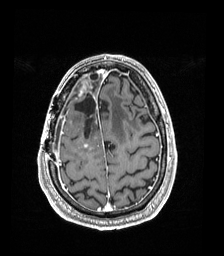
Brain MRI from a brain-tumour surgery series, one axial slice. Slice 45 of 192 in the series (ordered by position). T1-weighted post-contrast. 1 mm slice thickness. 224 × 256 image matrix. Case-level facts recorded for this patient, not image findings: histopathology: Astrocytoma; WHO grade: 4; IDH mutation: yes.
Structures marked on this image (expert manual segmentation):
- previous resection cavity: bounding box (x1, y1, x2, y2) in pixels: (75, 93, 96, 135)
- tumour: (79, 82, 89, 95)